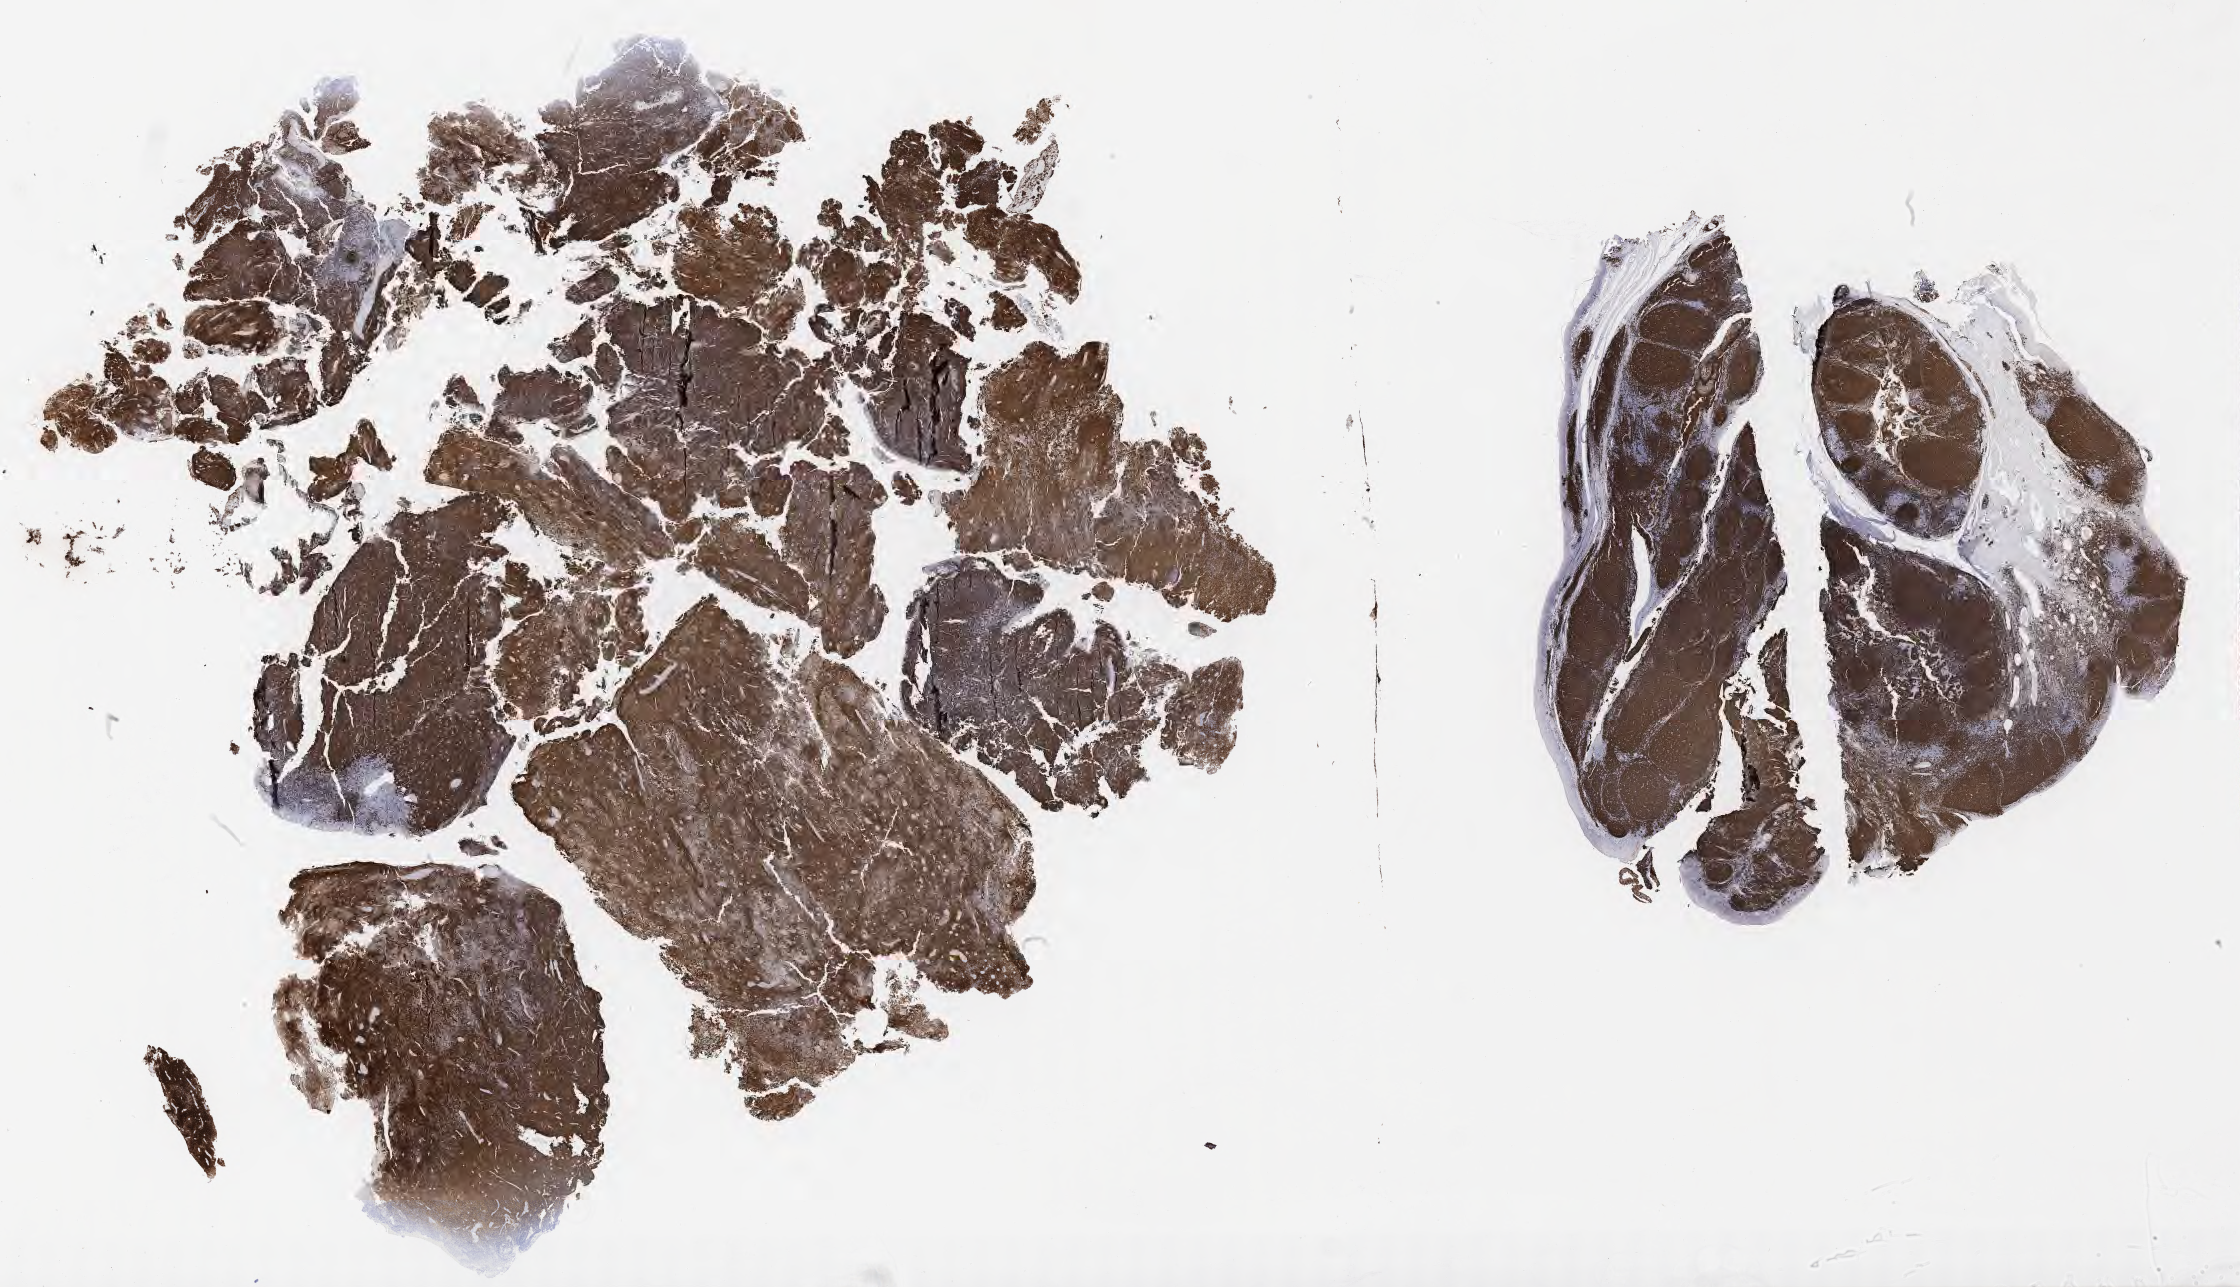
Immunohistochemistry (IHC) whole-slide image stained for CD20, low-resolution overview of the scanned area, about 36.2 x 20.8 mm; tumor tissue. Male patient, age 47 years.
* diagnosis: Diffuse large B-cell lymphoma, NOS